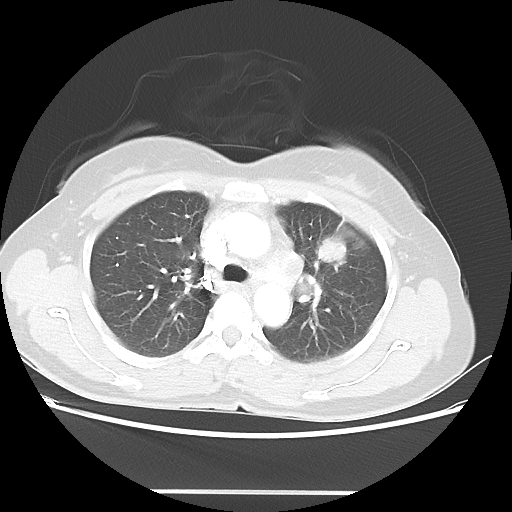
Chest CT, one axial slice. Slice 32 of 46 in the series (ordered by position). Reconstruction kernel LUNG. 100 kVp. Lung window (W 1500 / L -600 HU). 5 mm slice thickness. 512 × 512 image matrix, field of view 360 × 360 mm. Female patient, age 50 years. Case-level facts recorded for this patient, not image findings: clinical TNM (as recorded): T1c N1 M0.
Annotated regions visible in this slice (bounding box drawn by a radiologist):
- lung tumour (recorded histology: adenocarcinoma): bounding box <314,236,348,264> (left, top, right, bottom; pixels)